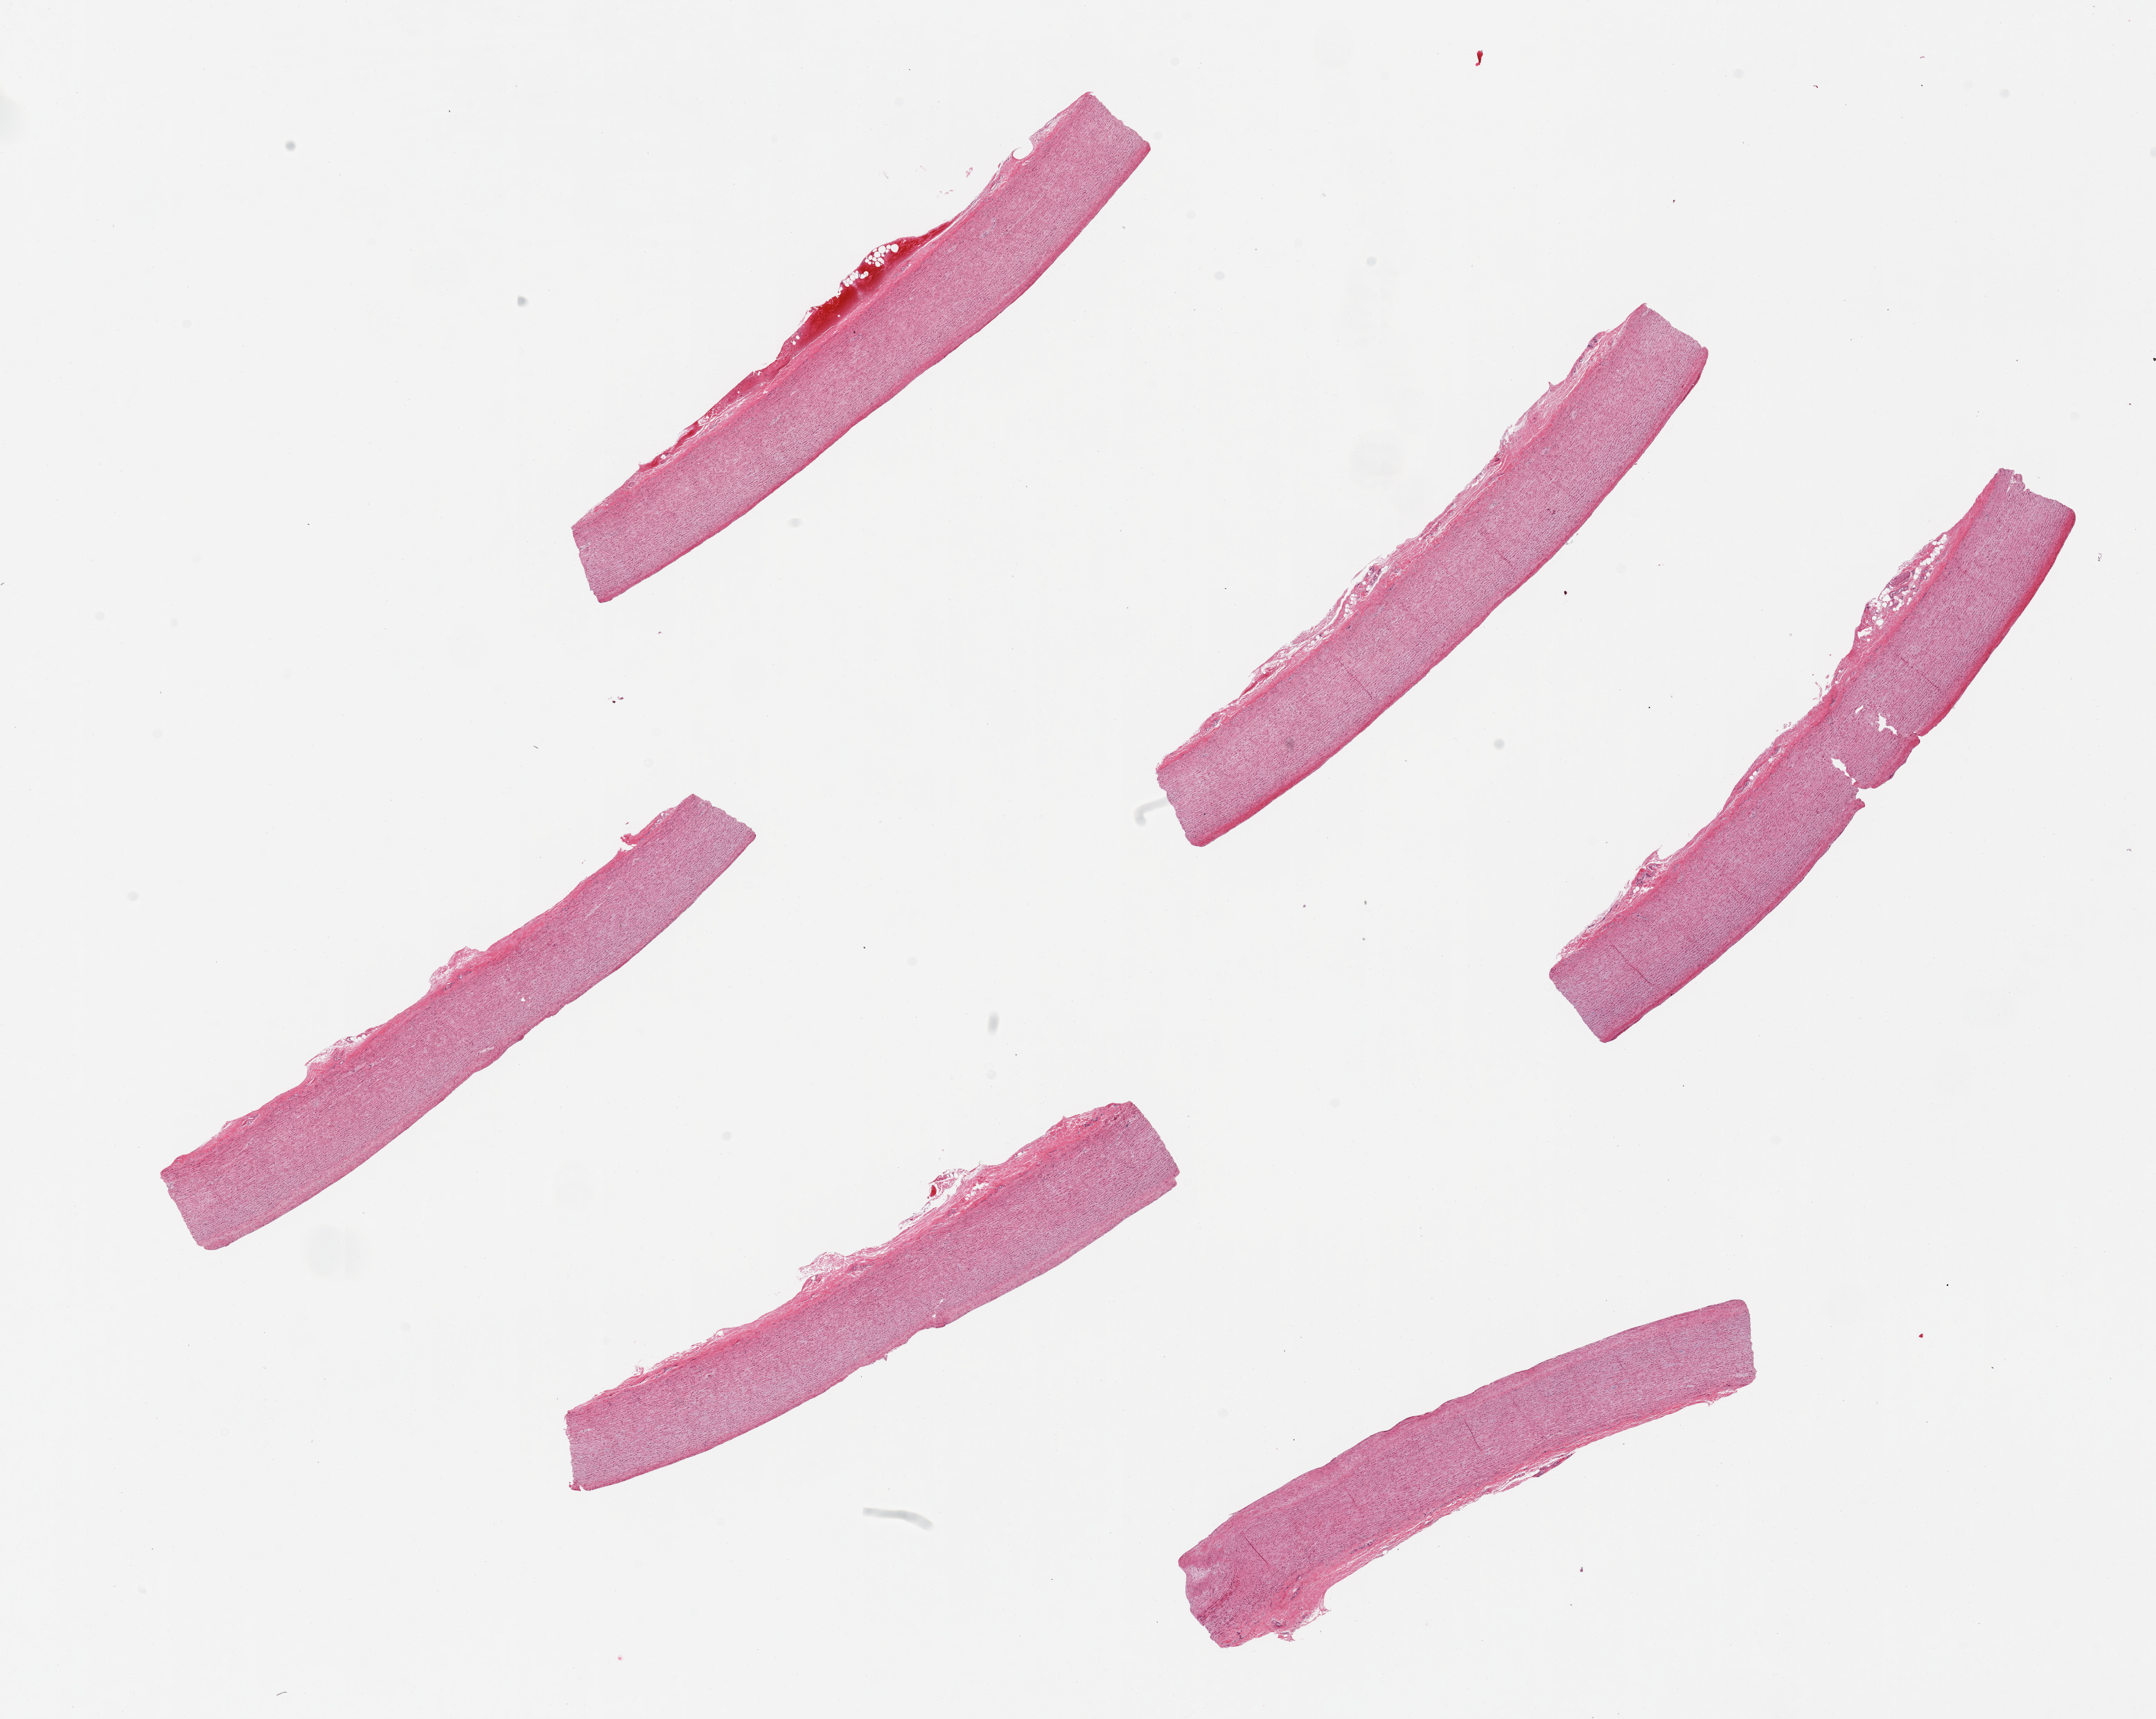
Digitized haematoxylin and eosin-stained section, brightfield — shown as a low-resolution overview of the whole scanned area (about 24.6 x 19.6 mm, acquisition: 20x scan). PAXgene-fixed, paraffin-embedded tissue. Sampled site (target tissue): aorta. Tissue donor sample. Donor sex: female.
Reviewer comment on this tissue sample: 6 pieces, minimal atherosis.